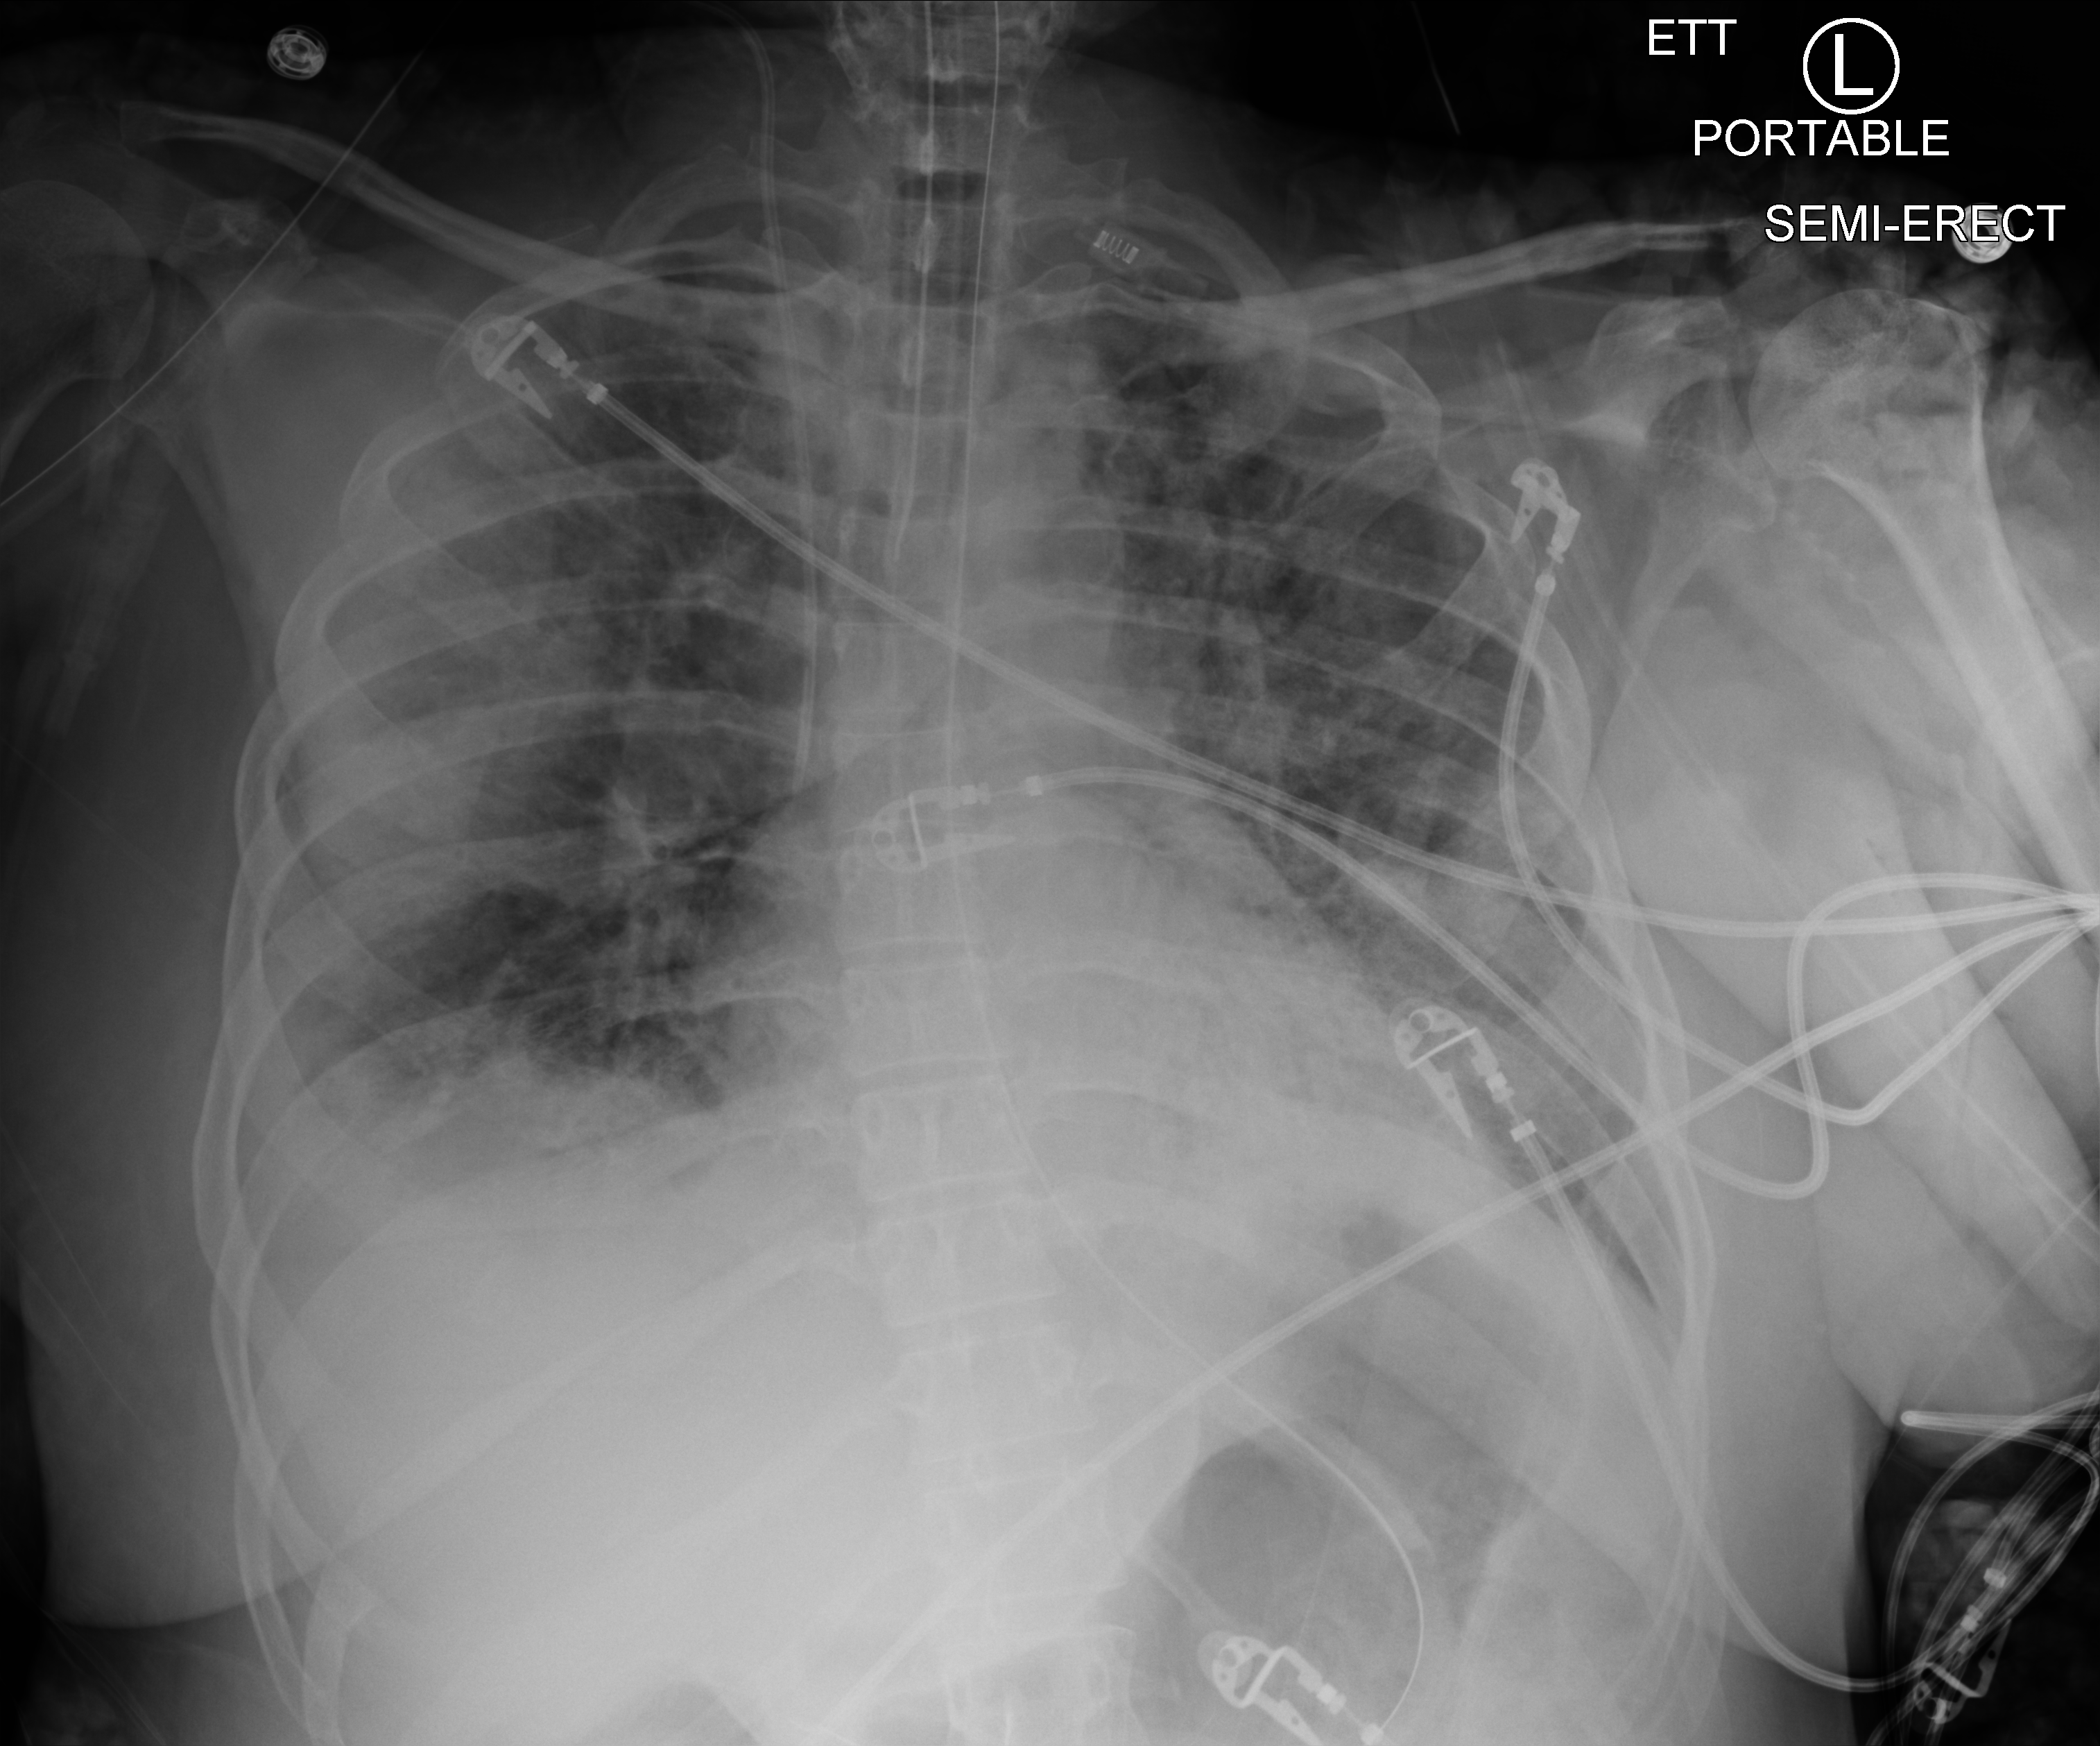
Bedside chest radiograph (computed radiography). Adult patient hospitalised with COVID-19, age 18–59 years.
Hospital-stay facts (about this admission, not read from this image; timing relative to this image not recorded):
- length of hospital stay: 15 days
- mechanically ventilated during this hospital stay: yes
- admitted to intensive care during this hospital stay: yes